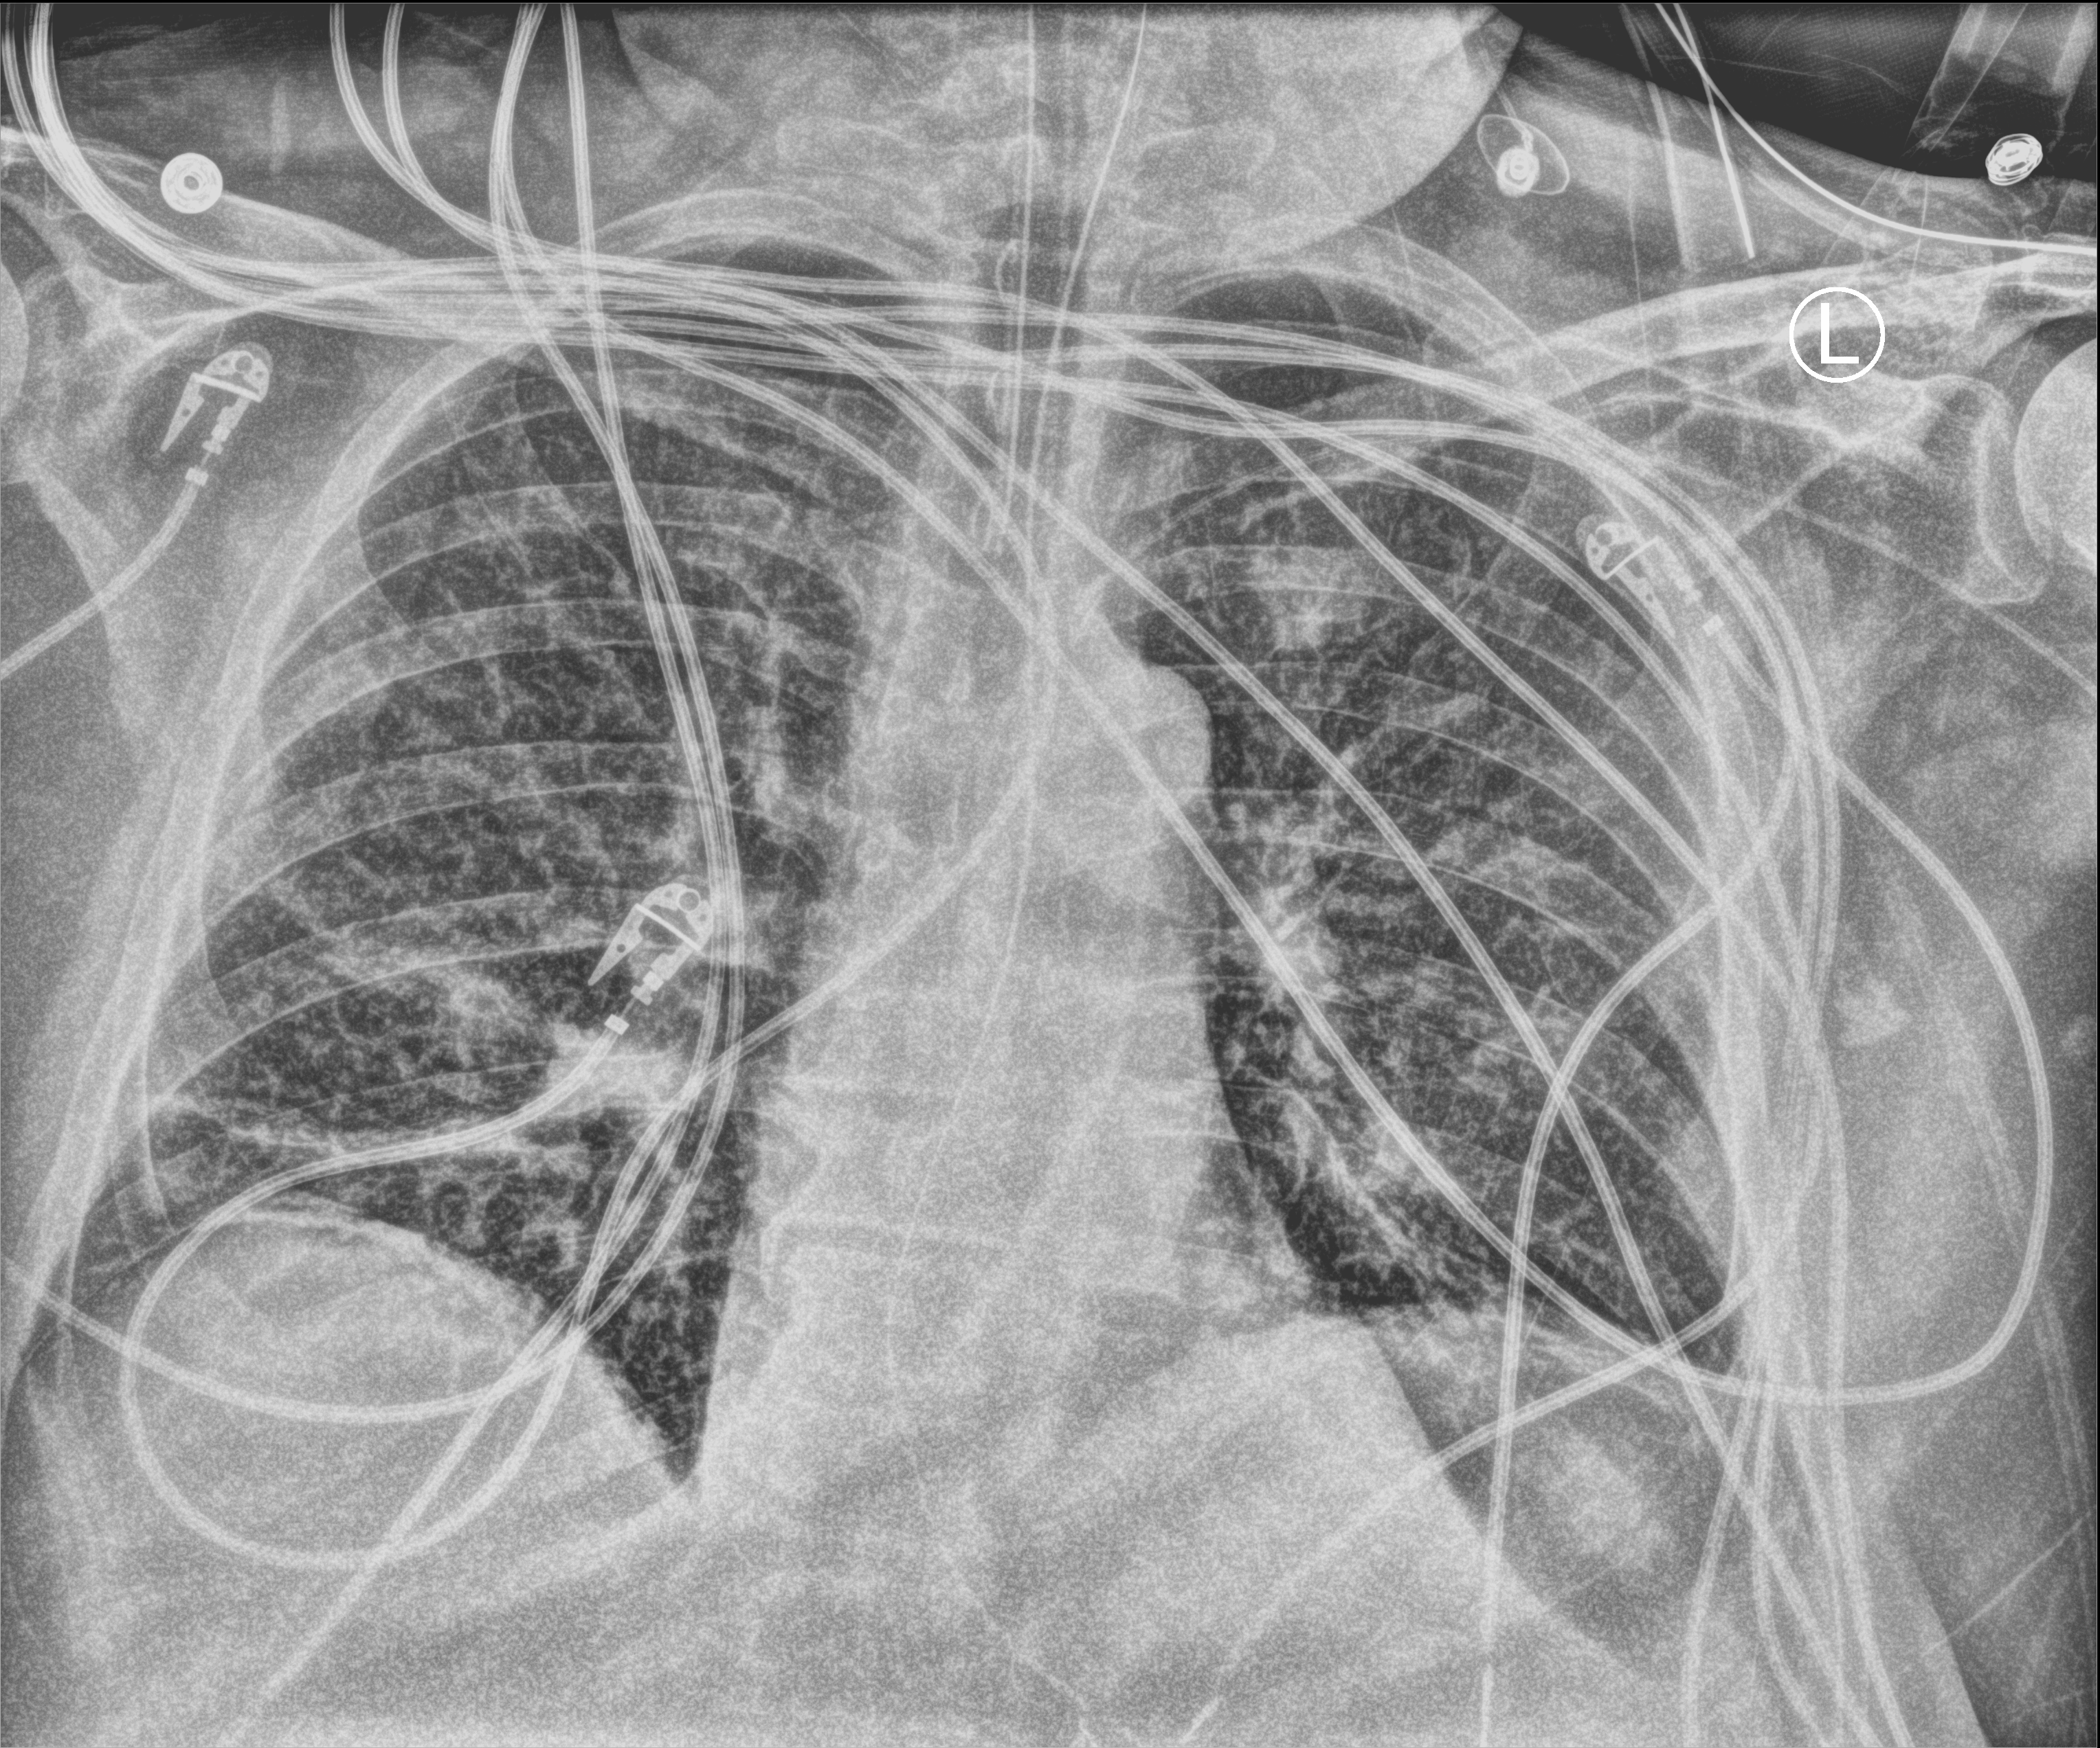
Portable chest radiograph, anteroposterior (AP) projection. Patient hospitalised with COVID-19; male, aged 60–74 years.
From the hospital-stay record, not from the radiograph (when in the stay this image was taken is not recorded): admitted to intensive care during this hospital stay: yes.